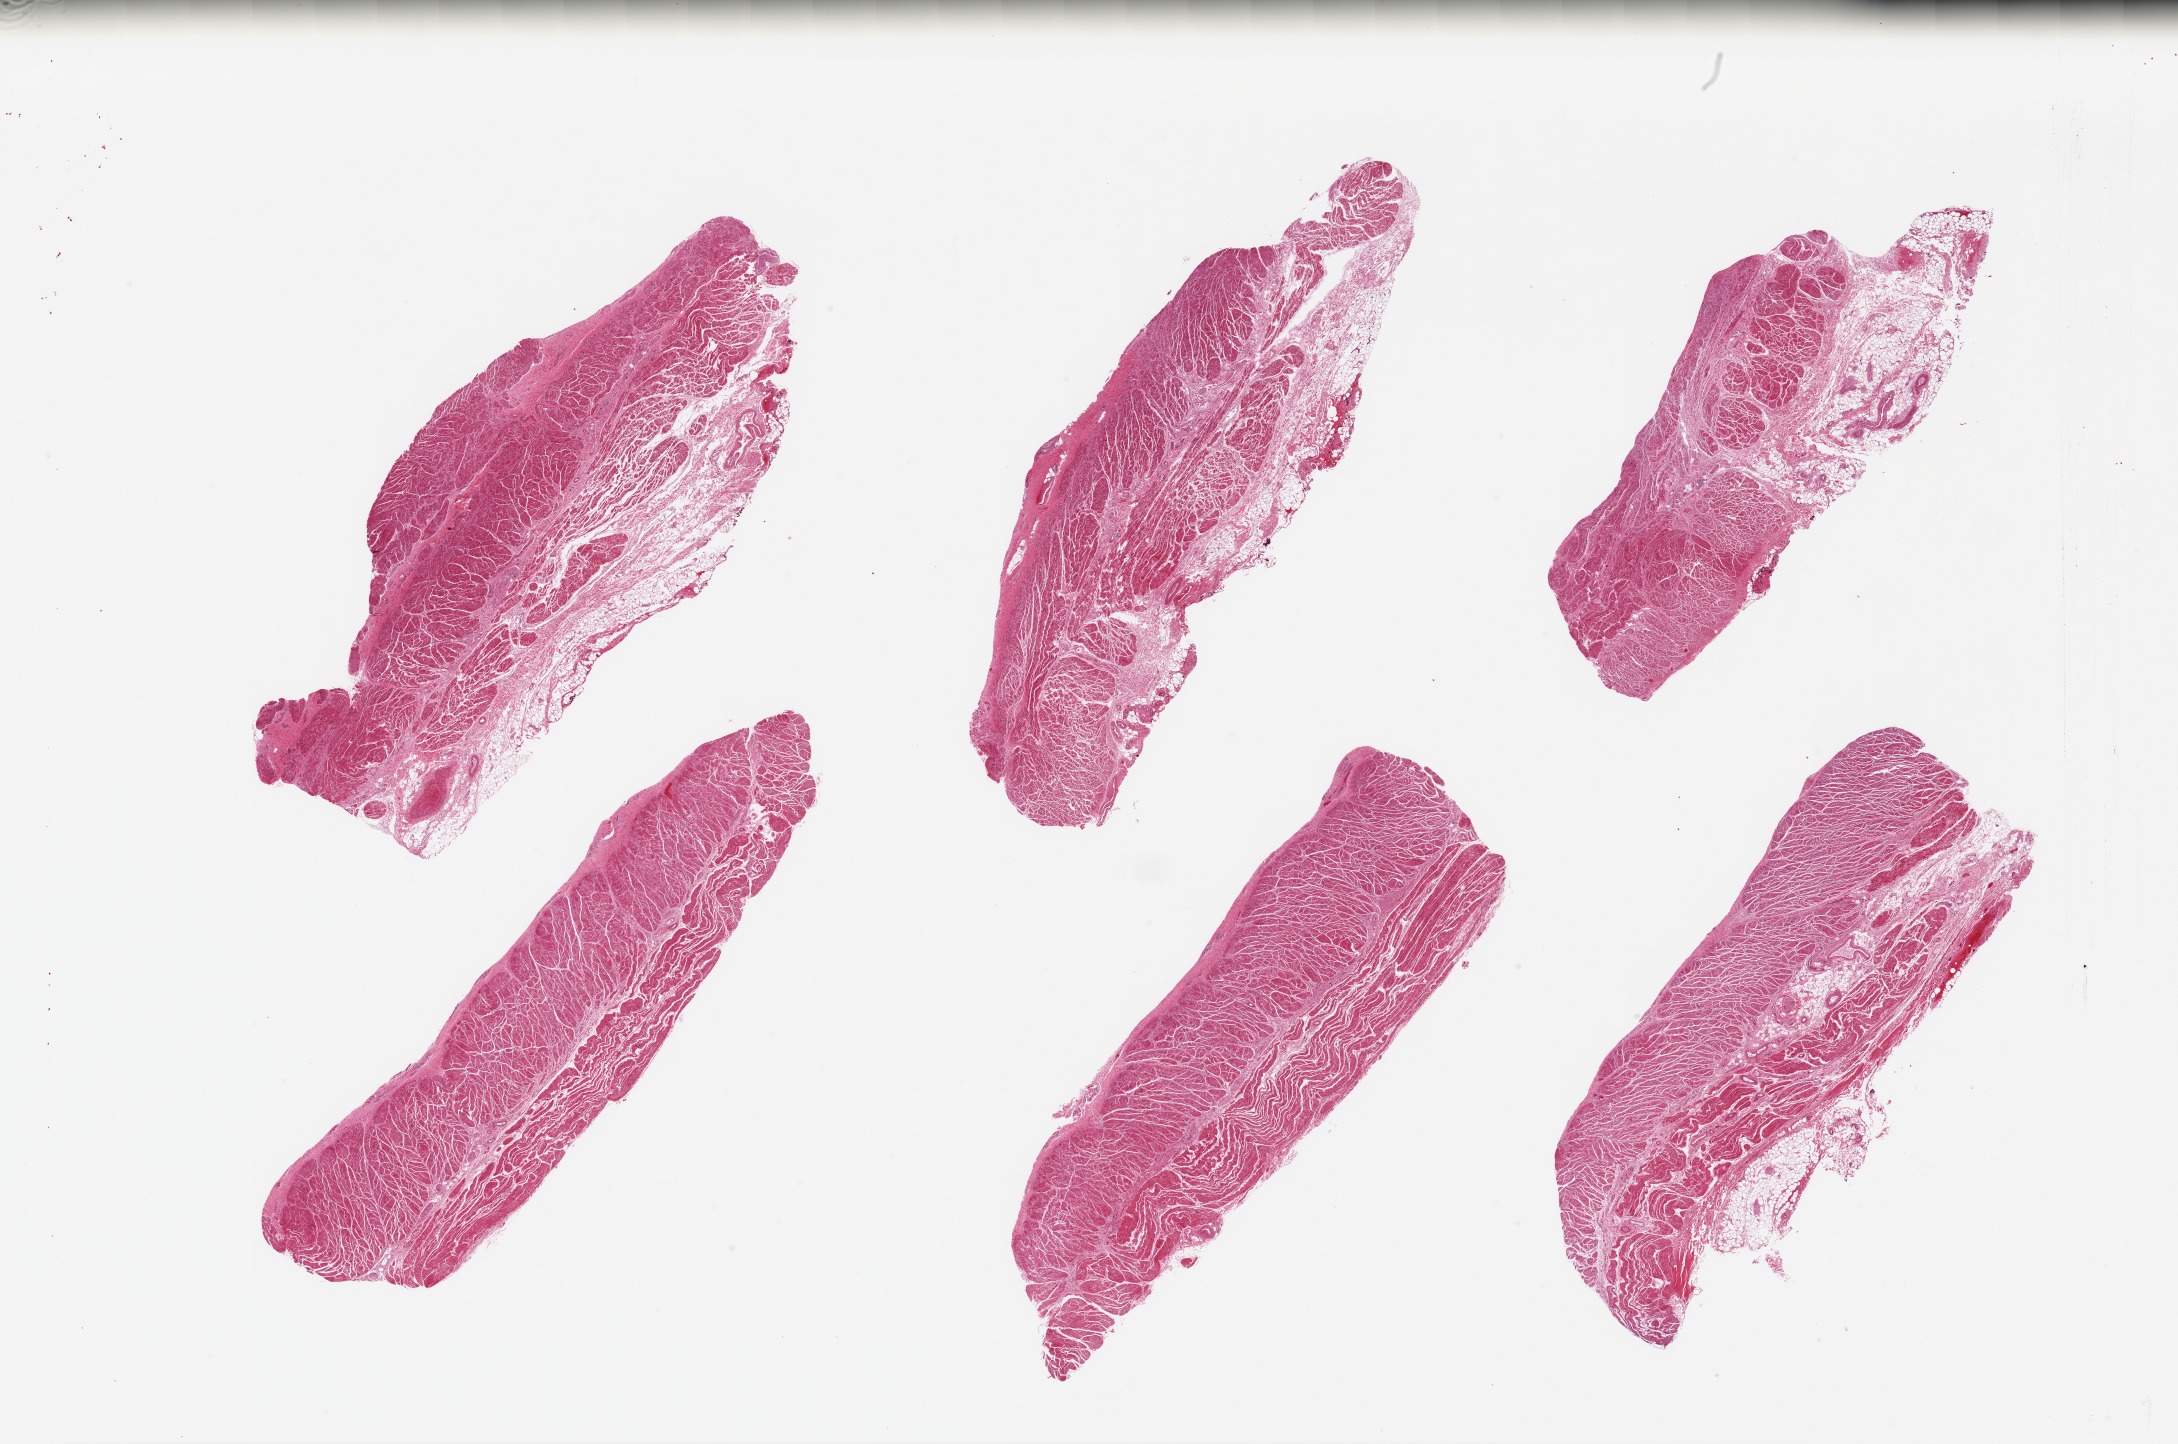
Haematoxylin and eosin whole-slide image, whole scanned area (about 34.5 x 22.8 mm) shown as a low-resolution overview, PAXgene-fixed paraffin-embedded (PFPE) section, target tissue: gastroesophageal junction, tissue donor sample. Donor sex: male.
• pathologist's review note for this sample: 6 pieces; 3 pieces have 30% fatty stroma